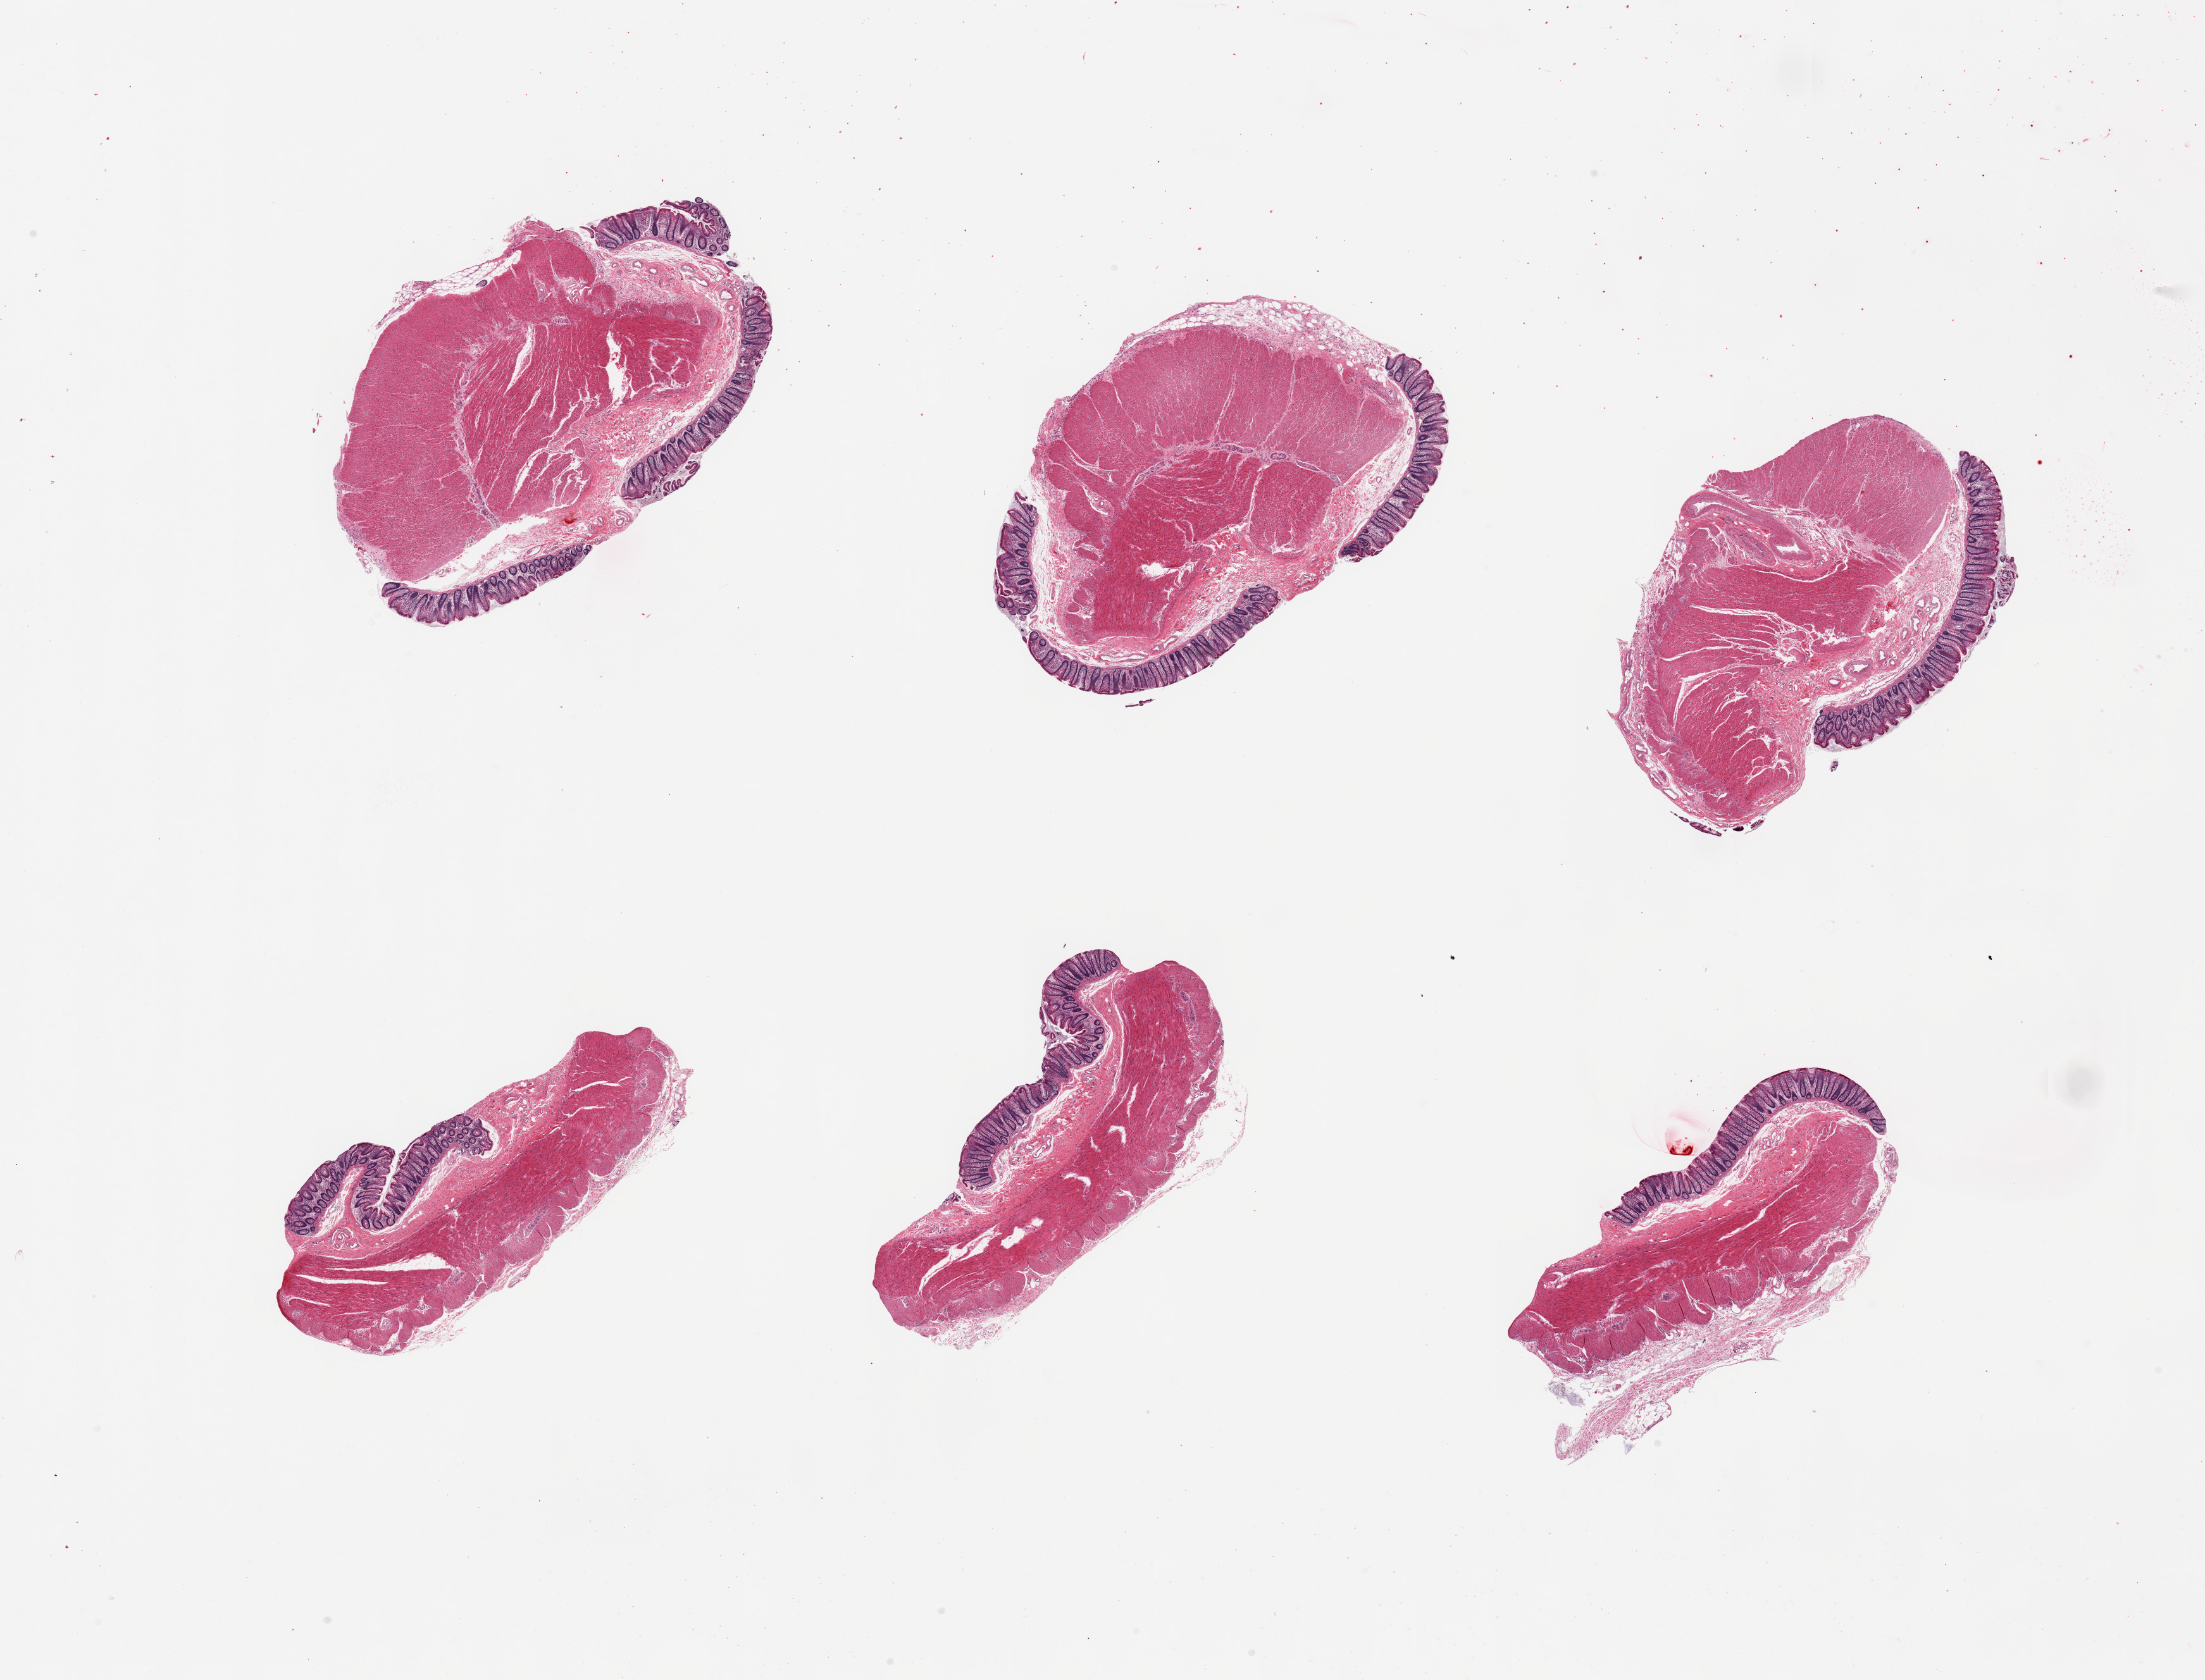
Digitized H&E-stained section — shown as a low-resolution overview of the whole scanned area (about 27.6 x 21.0 mm), PAXgene-fixed paraffin-embedded (PFPE) section, sampled site (target tissue): transverse colon, donor tissue sample. Donor sex: male.
Reviewer comment on this tissue sample: 6 pieces; well preserved. well trimmed.